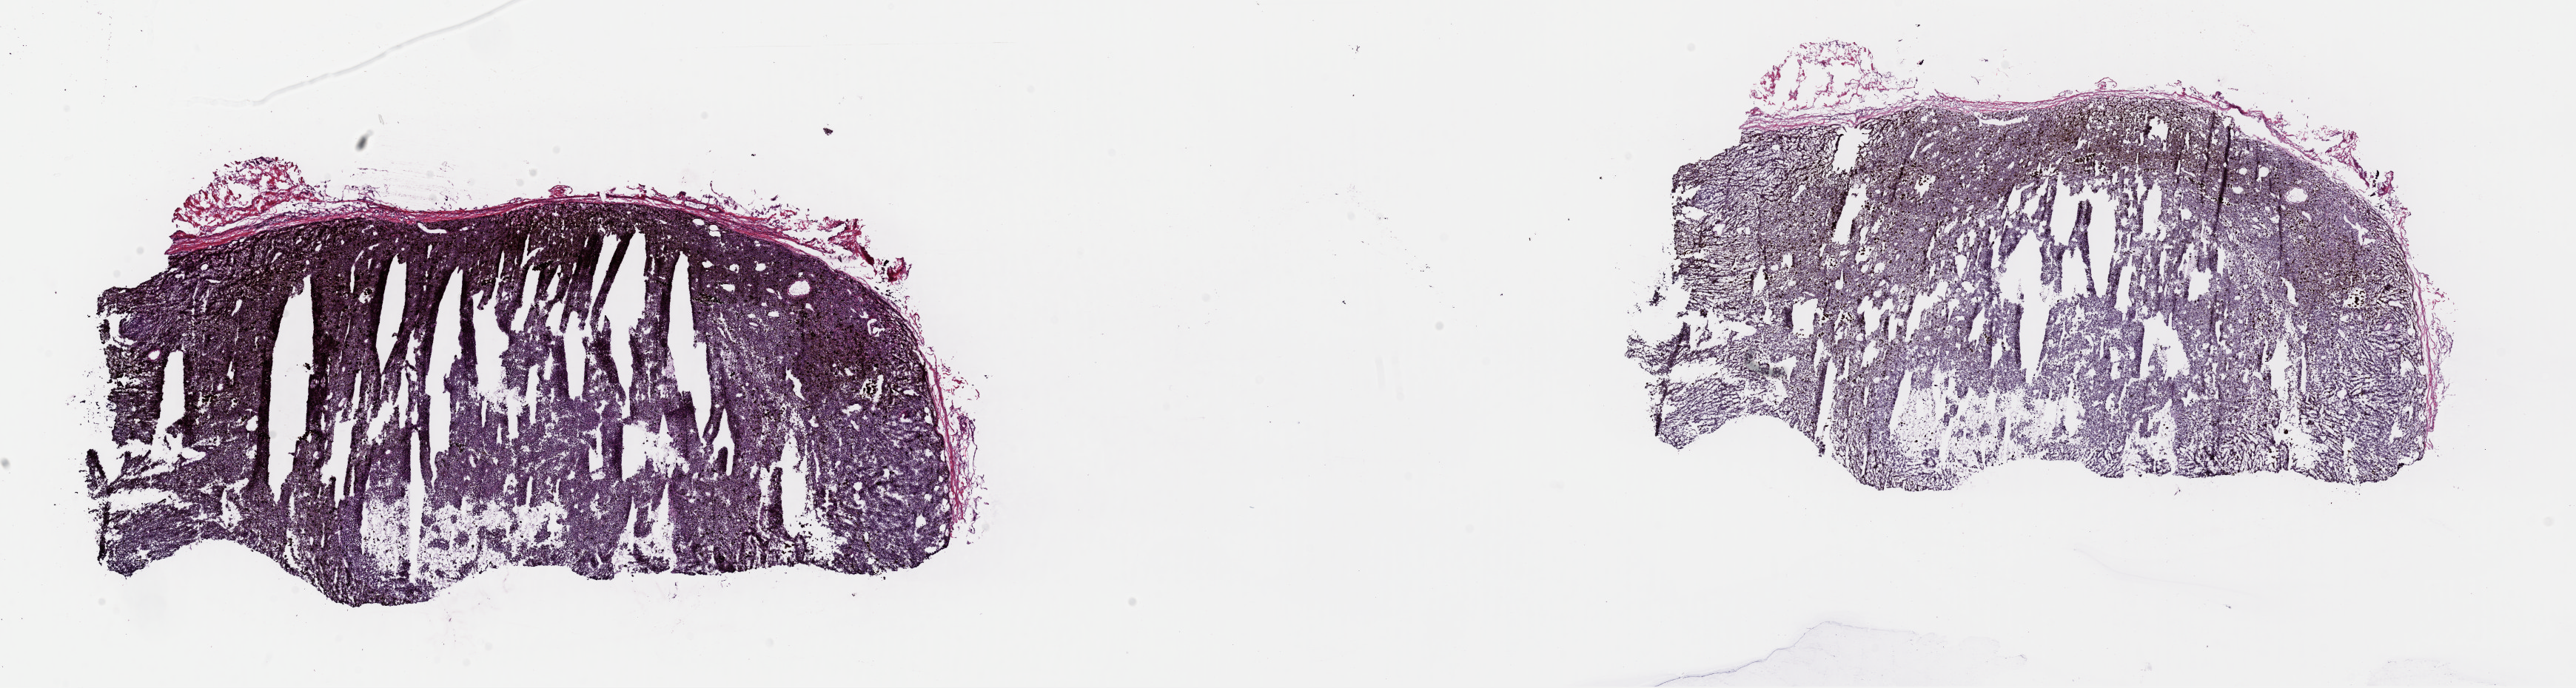
Whole-slide histology image, H&E, shown as a low-resolution overview of the whole scanned area (about 27.5 x 7.3 mm, slide scanned at 40x), frozen section from the top of the tissue portion, metastatic tumour sample, sampled site: lymph node. Male, age 52 years at initial diagnosis. Slide review estimates, as recorded: tumour cells 98%, tumour nuclei 96%, normal cells 0%, stromal cells 2%, necrosis 0%. Infiltration values recorded for this section: lymphocyte infiltration 0%, monocyte infiltration 0%, neutrophil infiltration 0%.
This section: metastatic tumour tissue. Patient diagnosis: Malignant melanoma, NOS.